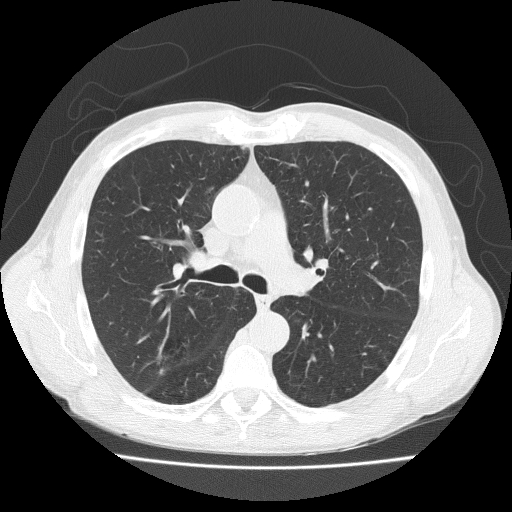
Chest CT (low-dose screening protocol), one axial image. Baseline screening round. Lung window (W 1500 / L -600 HU). 2 mm slice thickness. Lung (sharp) reconstruction kernel (FC51). 120 kVp. Slice 77 of 203 in the series. Male participant, aged 73 years at enrolment. Current smoker at enrolment.
Expert-annotated lung lesion, bounding box <144,329,192,375> (left, top, right, bottom; pixels). No non-calcified nodule or mass ≥4 mm was recorded by the screening reader at this exam. Participant outcome: lung cancer diagnosed 777 days after this screen — adenosquamous carcinoma, right upper lobe, well differentiated (G1), stage IA (AJCC 6th edition), 20 mm at pathology.